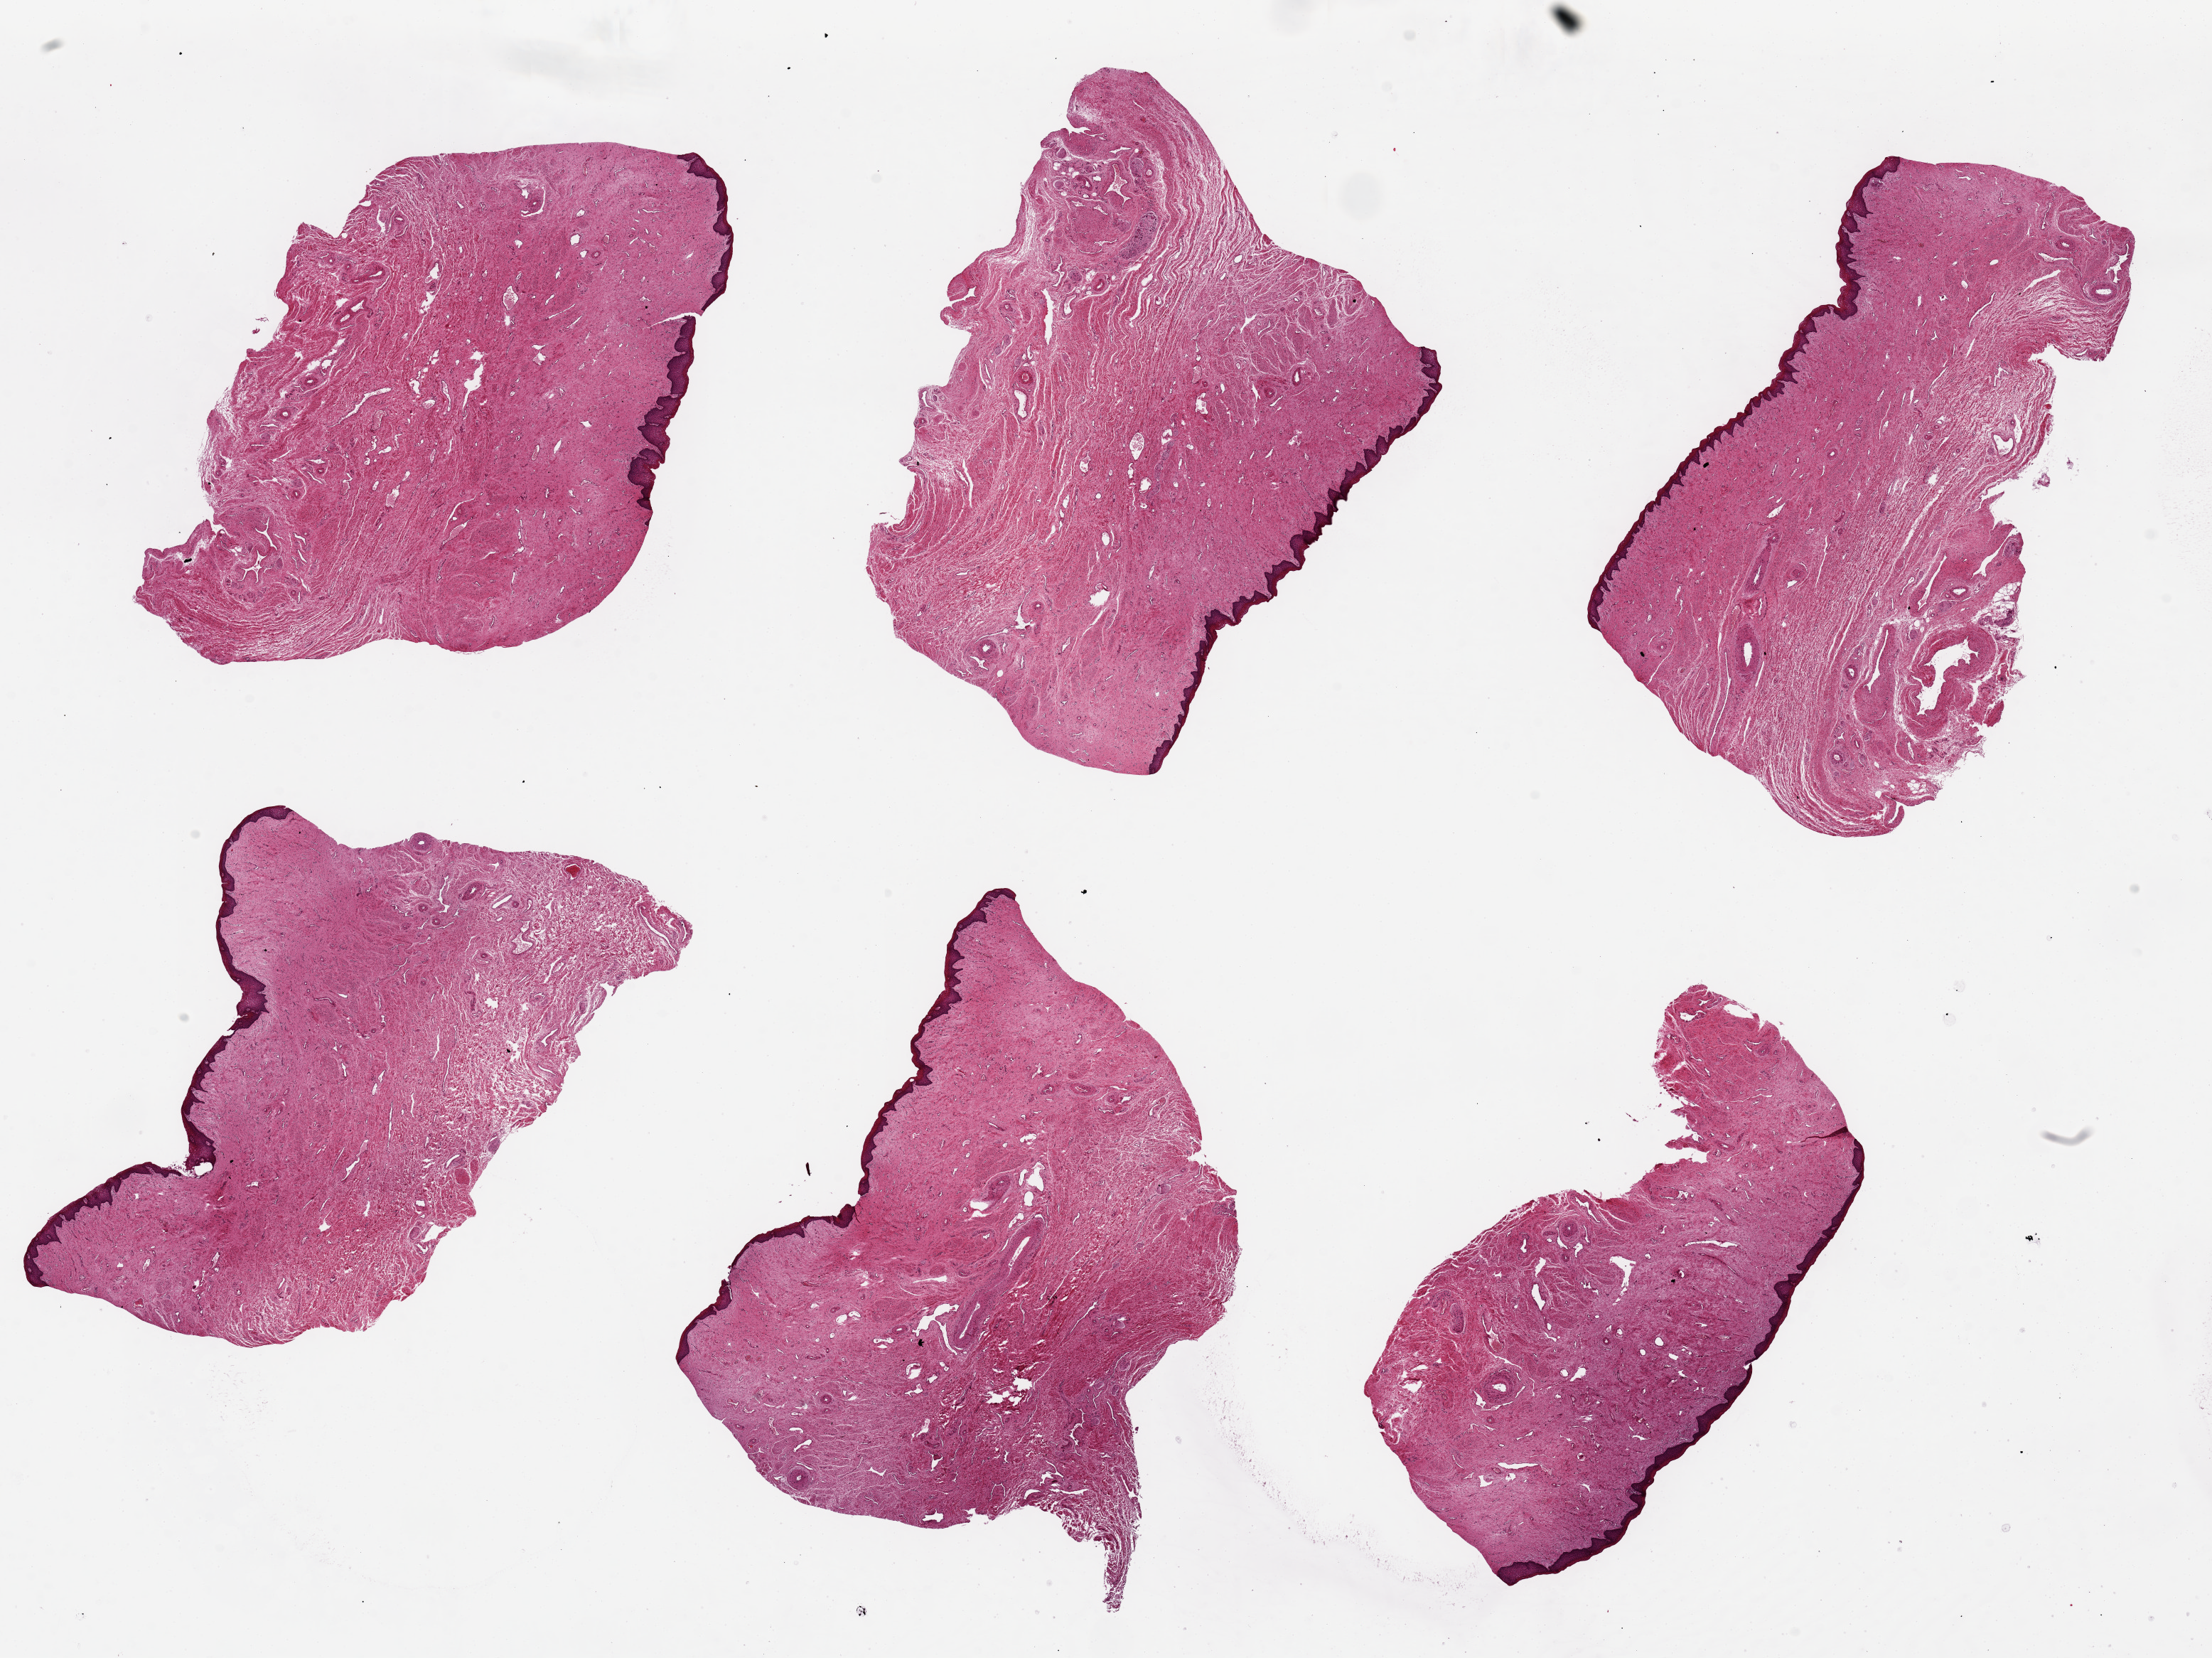
Haematoxylin and eosin whole-slide image — a low-resolution overview of the entire scanned area, about 24.6 x 18.4 mm (acquisition: 20x scan), PAXgene-fixed, paraffin-embedded tissue, sampled site (target tissue): vagina, tissue donor sample. Donor: female.
Review note (as recorded): 6 pieces ~5x5mm. Squamous mucosa is ~3-5% of thickness.